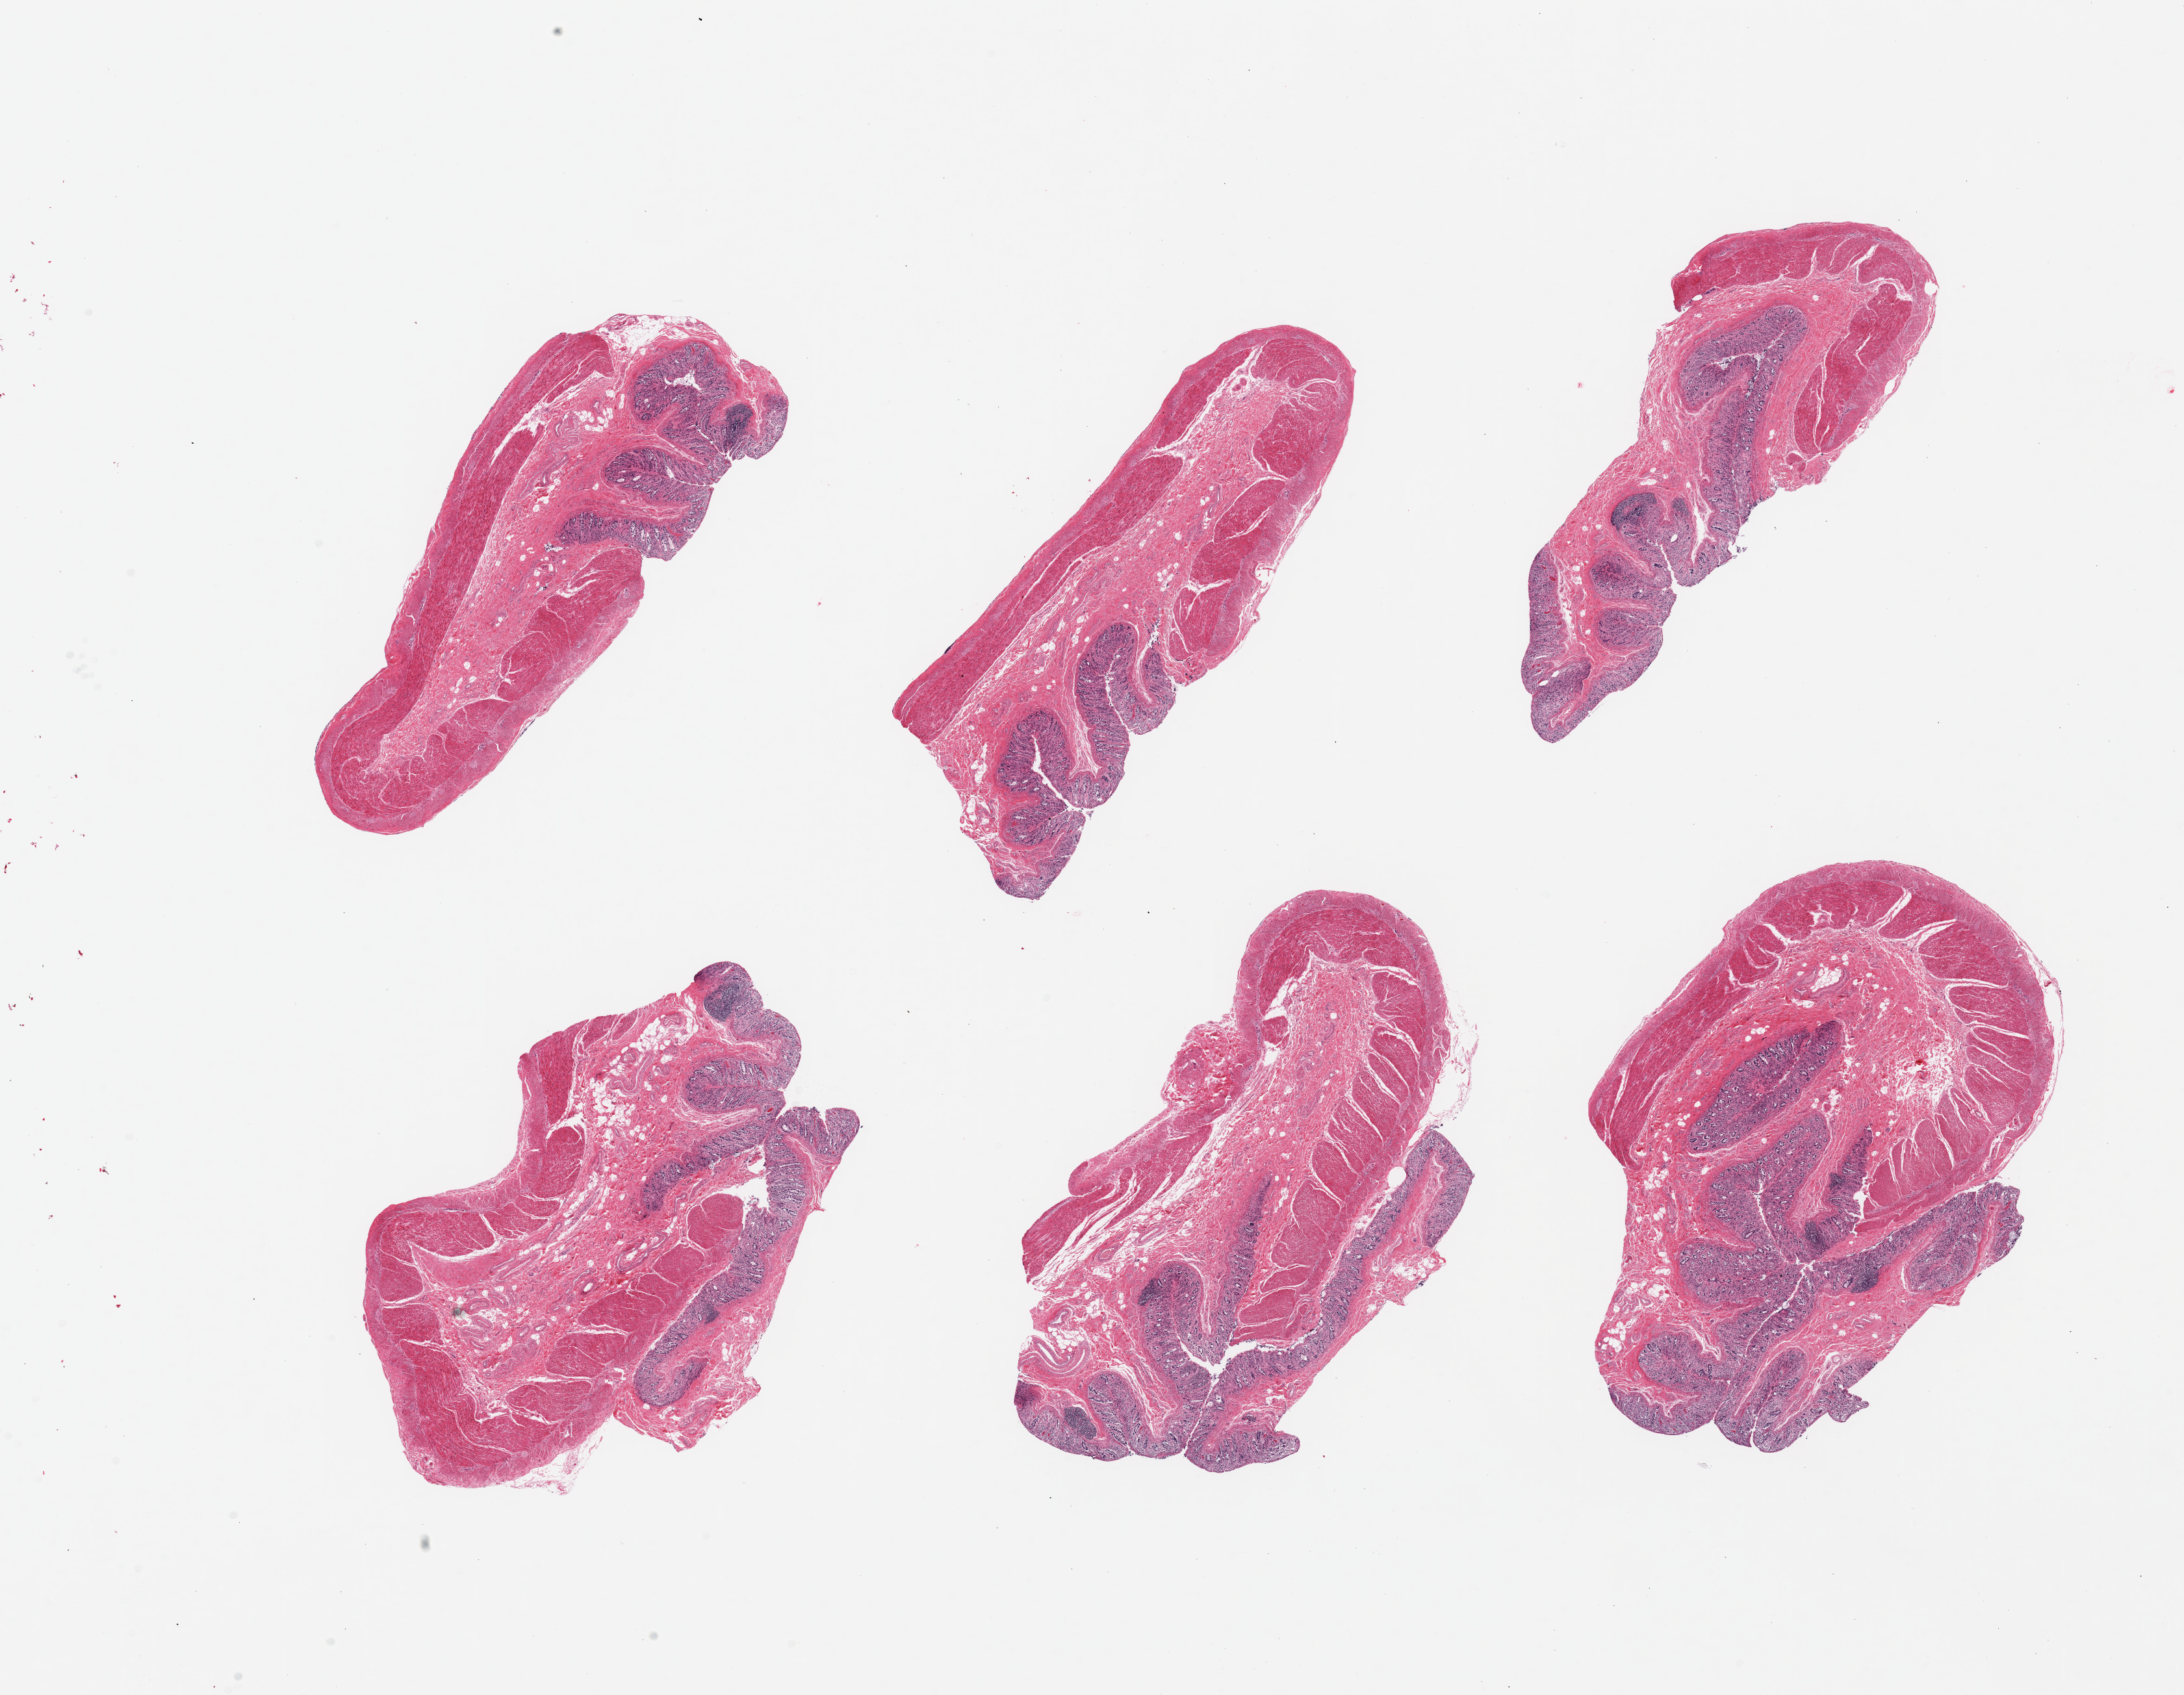
Hematoxylin and eosin (H&E) whole-slide image — shown as a low-resolution overview of the whole scanned area (about 26.6 x 20.6 mm). PAXgene-fixed paraffin-embedded (PFPE) section. Target tissue: transverse colon. Donor tissue sample. Male donor.
• reviewer comment on this tissue sample: 6 pieces, target mucosa up to ~0.4mm, ~20-25% thickness. Glandular elements sloughed, lamina propria only